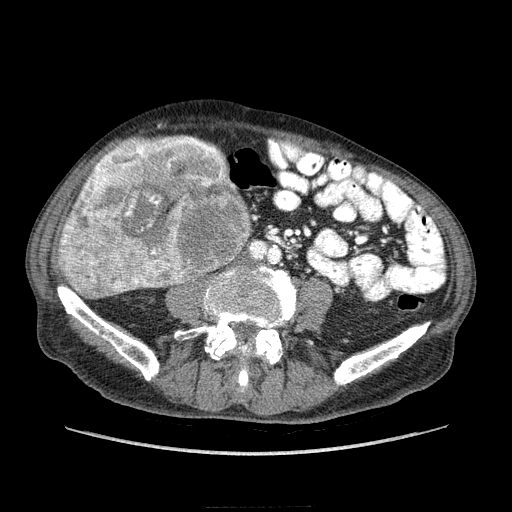
Contrast-enhanced abdominal CT (liver protocol), one axial slice. Position 45 of 218 along the scan axis. 100 kVp. Soft-tissue window (W 400 / L 40 HU). 2.5 mm slice thickness. 512 × 512 image matrix, field of view 380 × 380 mm. From the clinical record (not read from this slice): diagnosis: hepatocellular carcinoma (patient treated with transarterial chemoembolisation; whether this scan precedes or follows treatment is not stated here); TNM stage (as recorded): Stage-IIIA; Child-Pugh class: A; tumour differentiation: well differentiated; tumour size: 20 cm.
Annotated regions visible in this slice (semi-automatic segmentation, software-assisted and operator-edited):
- liver parenchyma outside the tumour (the mass and vessels are separate outlines, so this box may not span the whole liver): bounding box [x1, y1, x2, y2] px = [59, 159, 250, 298]
- mass: [59, 135, 250, 298]